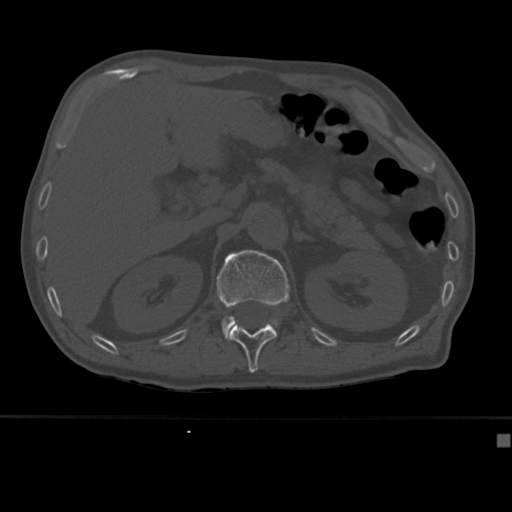
CT including the spine, one axial slice. Position 180 of 430 along the scan axis. 120 kVp. Bone window (W 1800 / L 400 HU). 512 × 512 image matrix. Male patient, age 64 years. Case-level facts recorded for this patient, not image findings: primary cancer: uterus.
Annotated regions visible in this slice (semi-automatic segmentation, software-assisted and operator-edited):
- L1 vertebra: bounding box (x1, y1, x2, y2) in pixels: (216, 250, 290, 340)
- T12 vertebra: (229, 324, 277, 373)